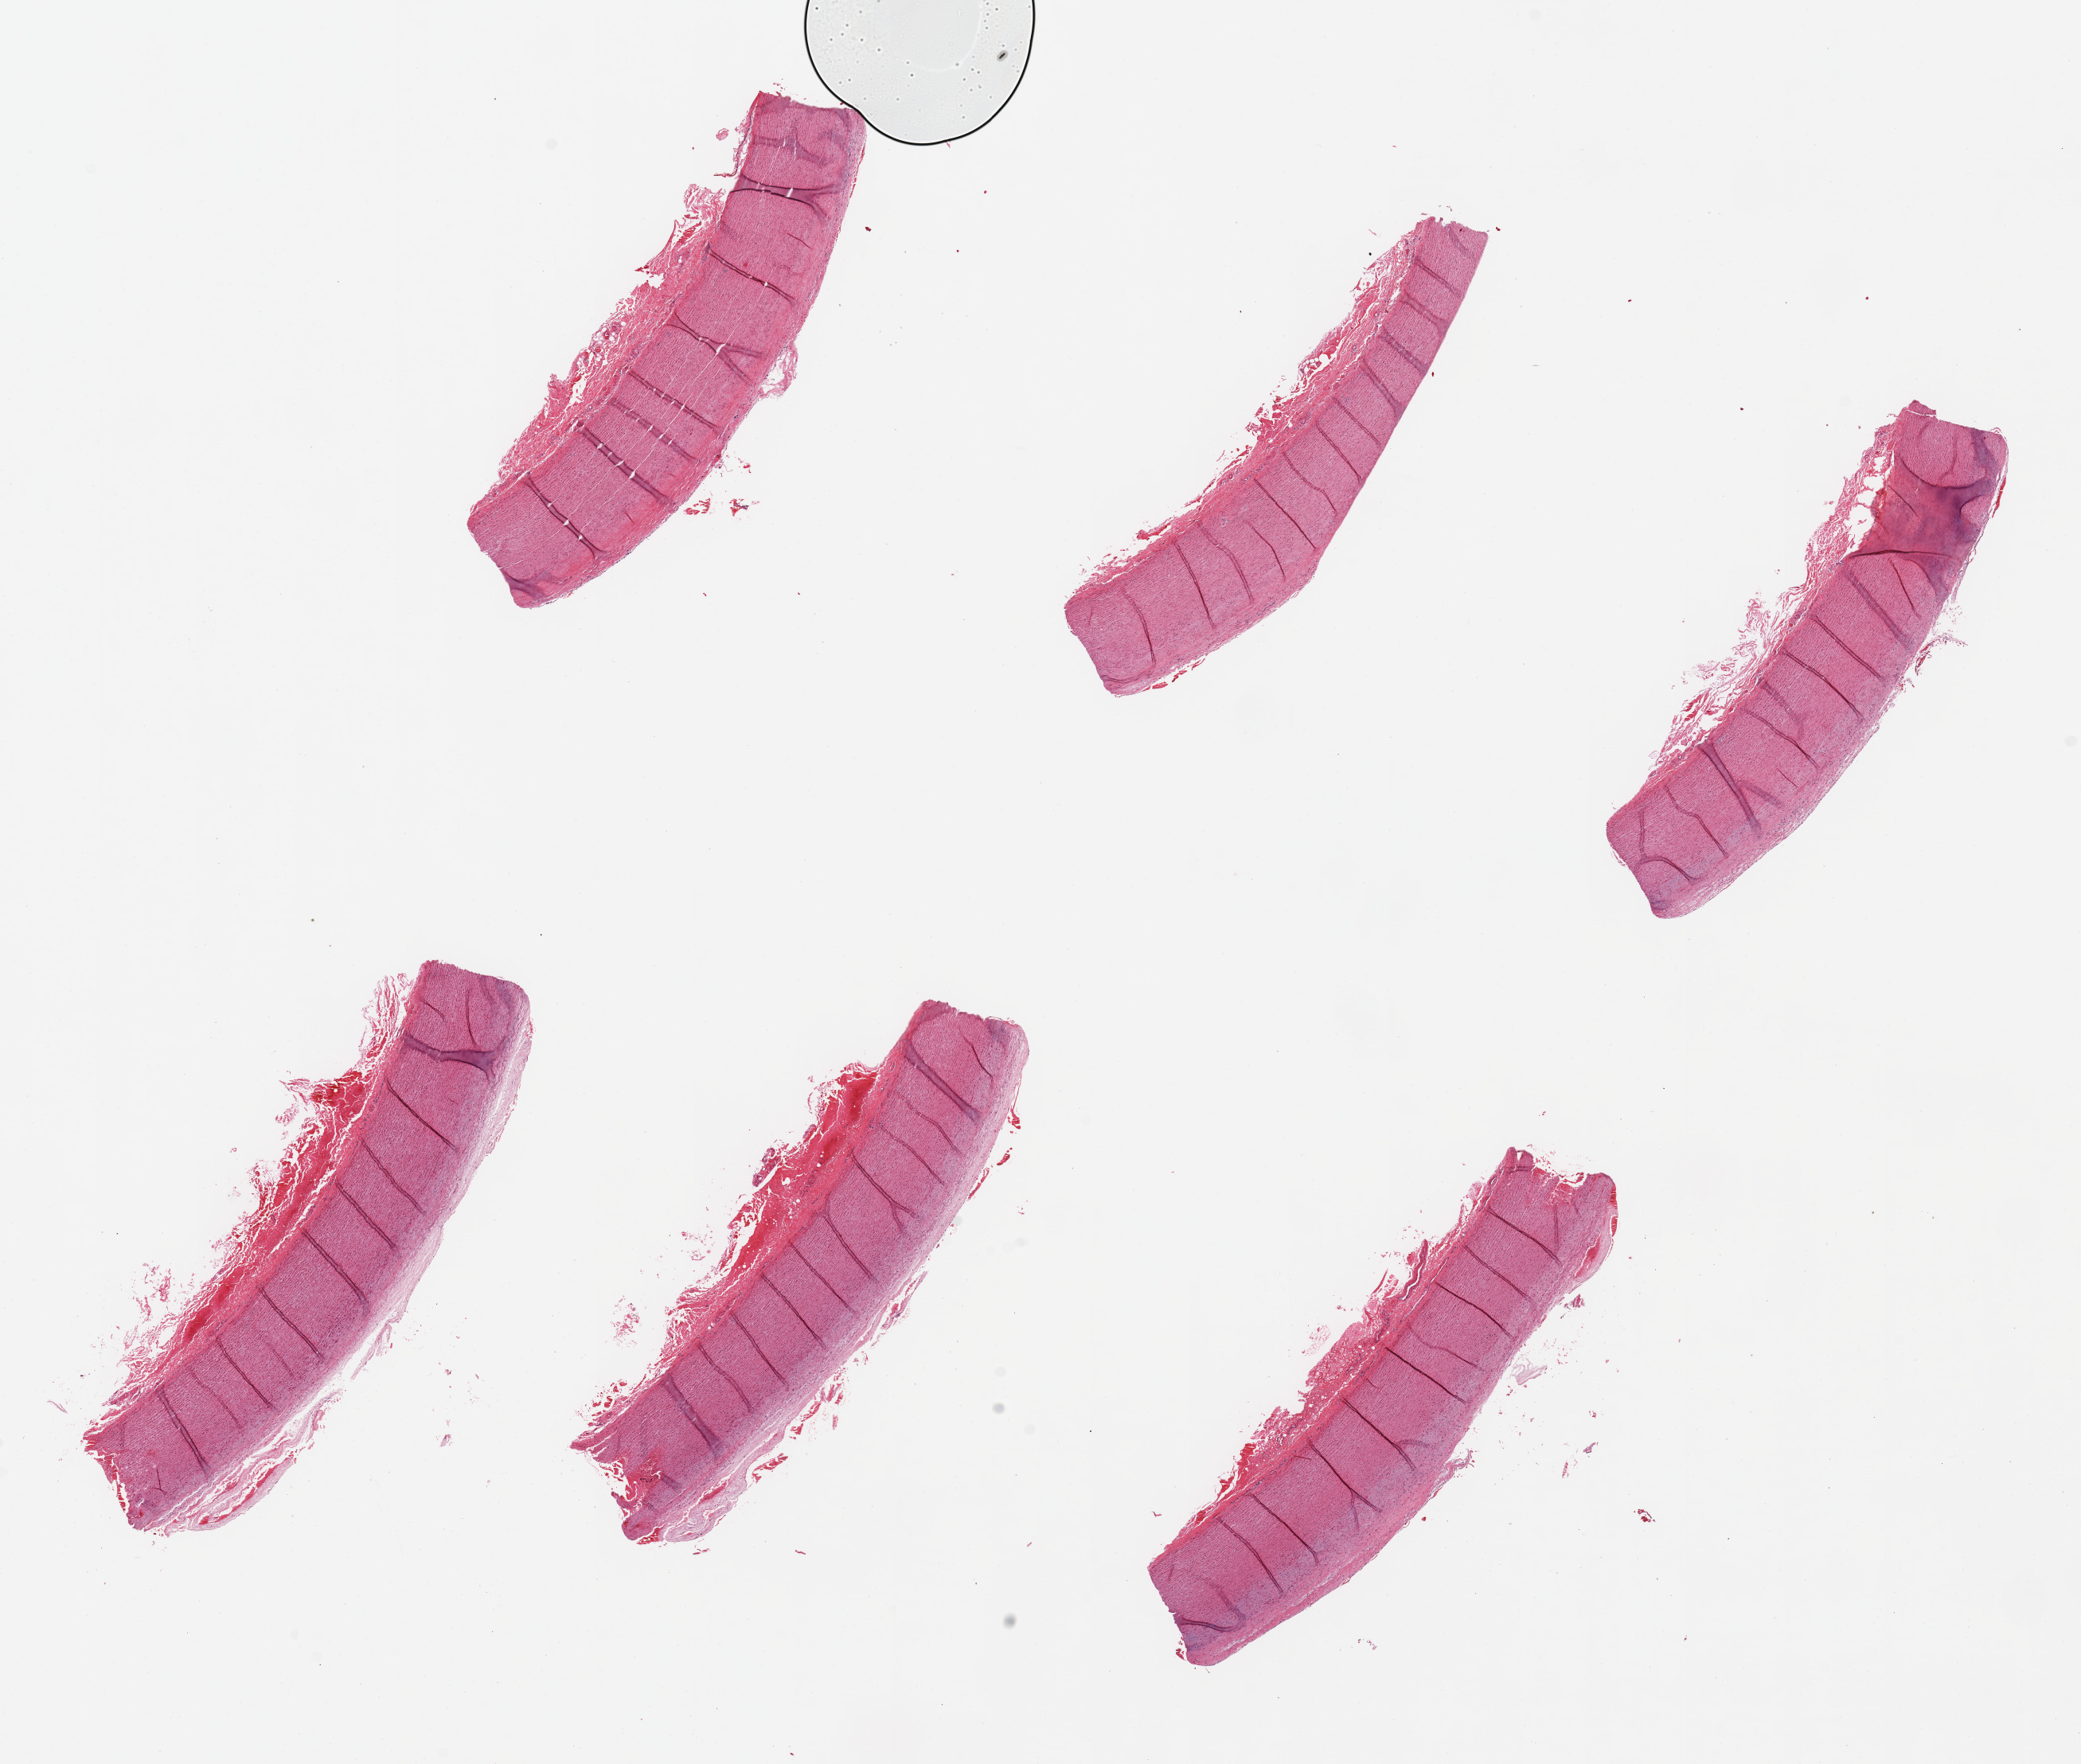
Whole-slide image, haematoxylin and eosin stain, low-resolution overview of the scanned area, about 20.7 x 17.5 mm; PAXgene-fixed paraffin-embedded (PFPE) section; target tissue: aorta; donor tissue sample. Male donor.
Reviewer comment on this tissue sample: 6 pieces, up to 7x2.5mm; uniform fibrous intimal plaques; fibrous adventitia up to 0.5 mm.